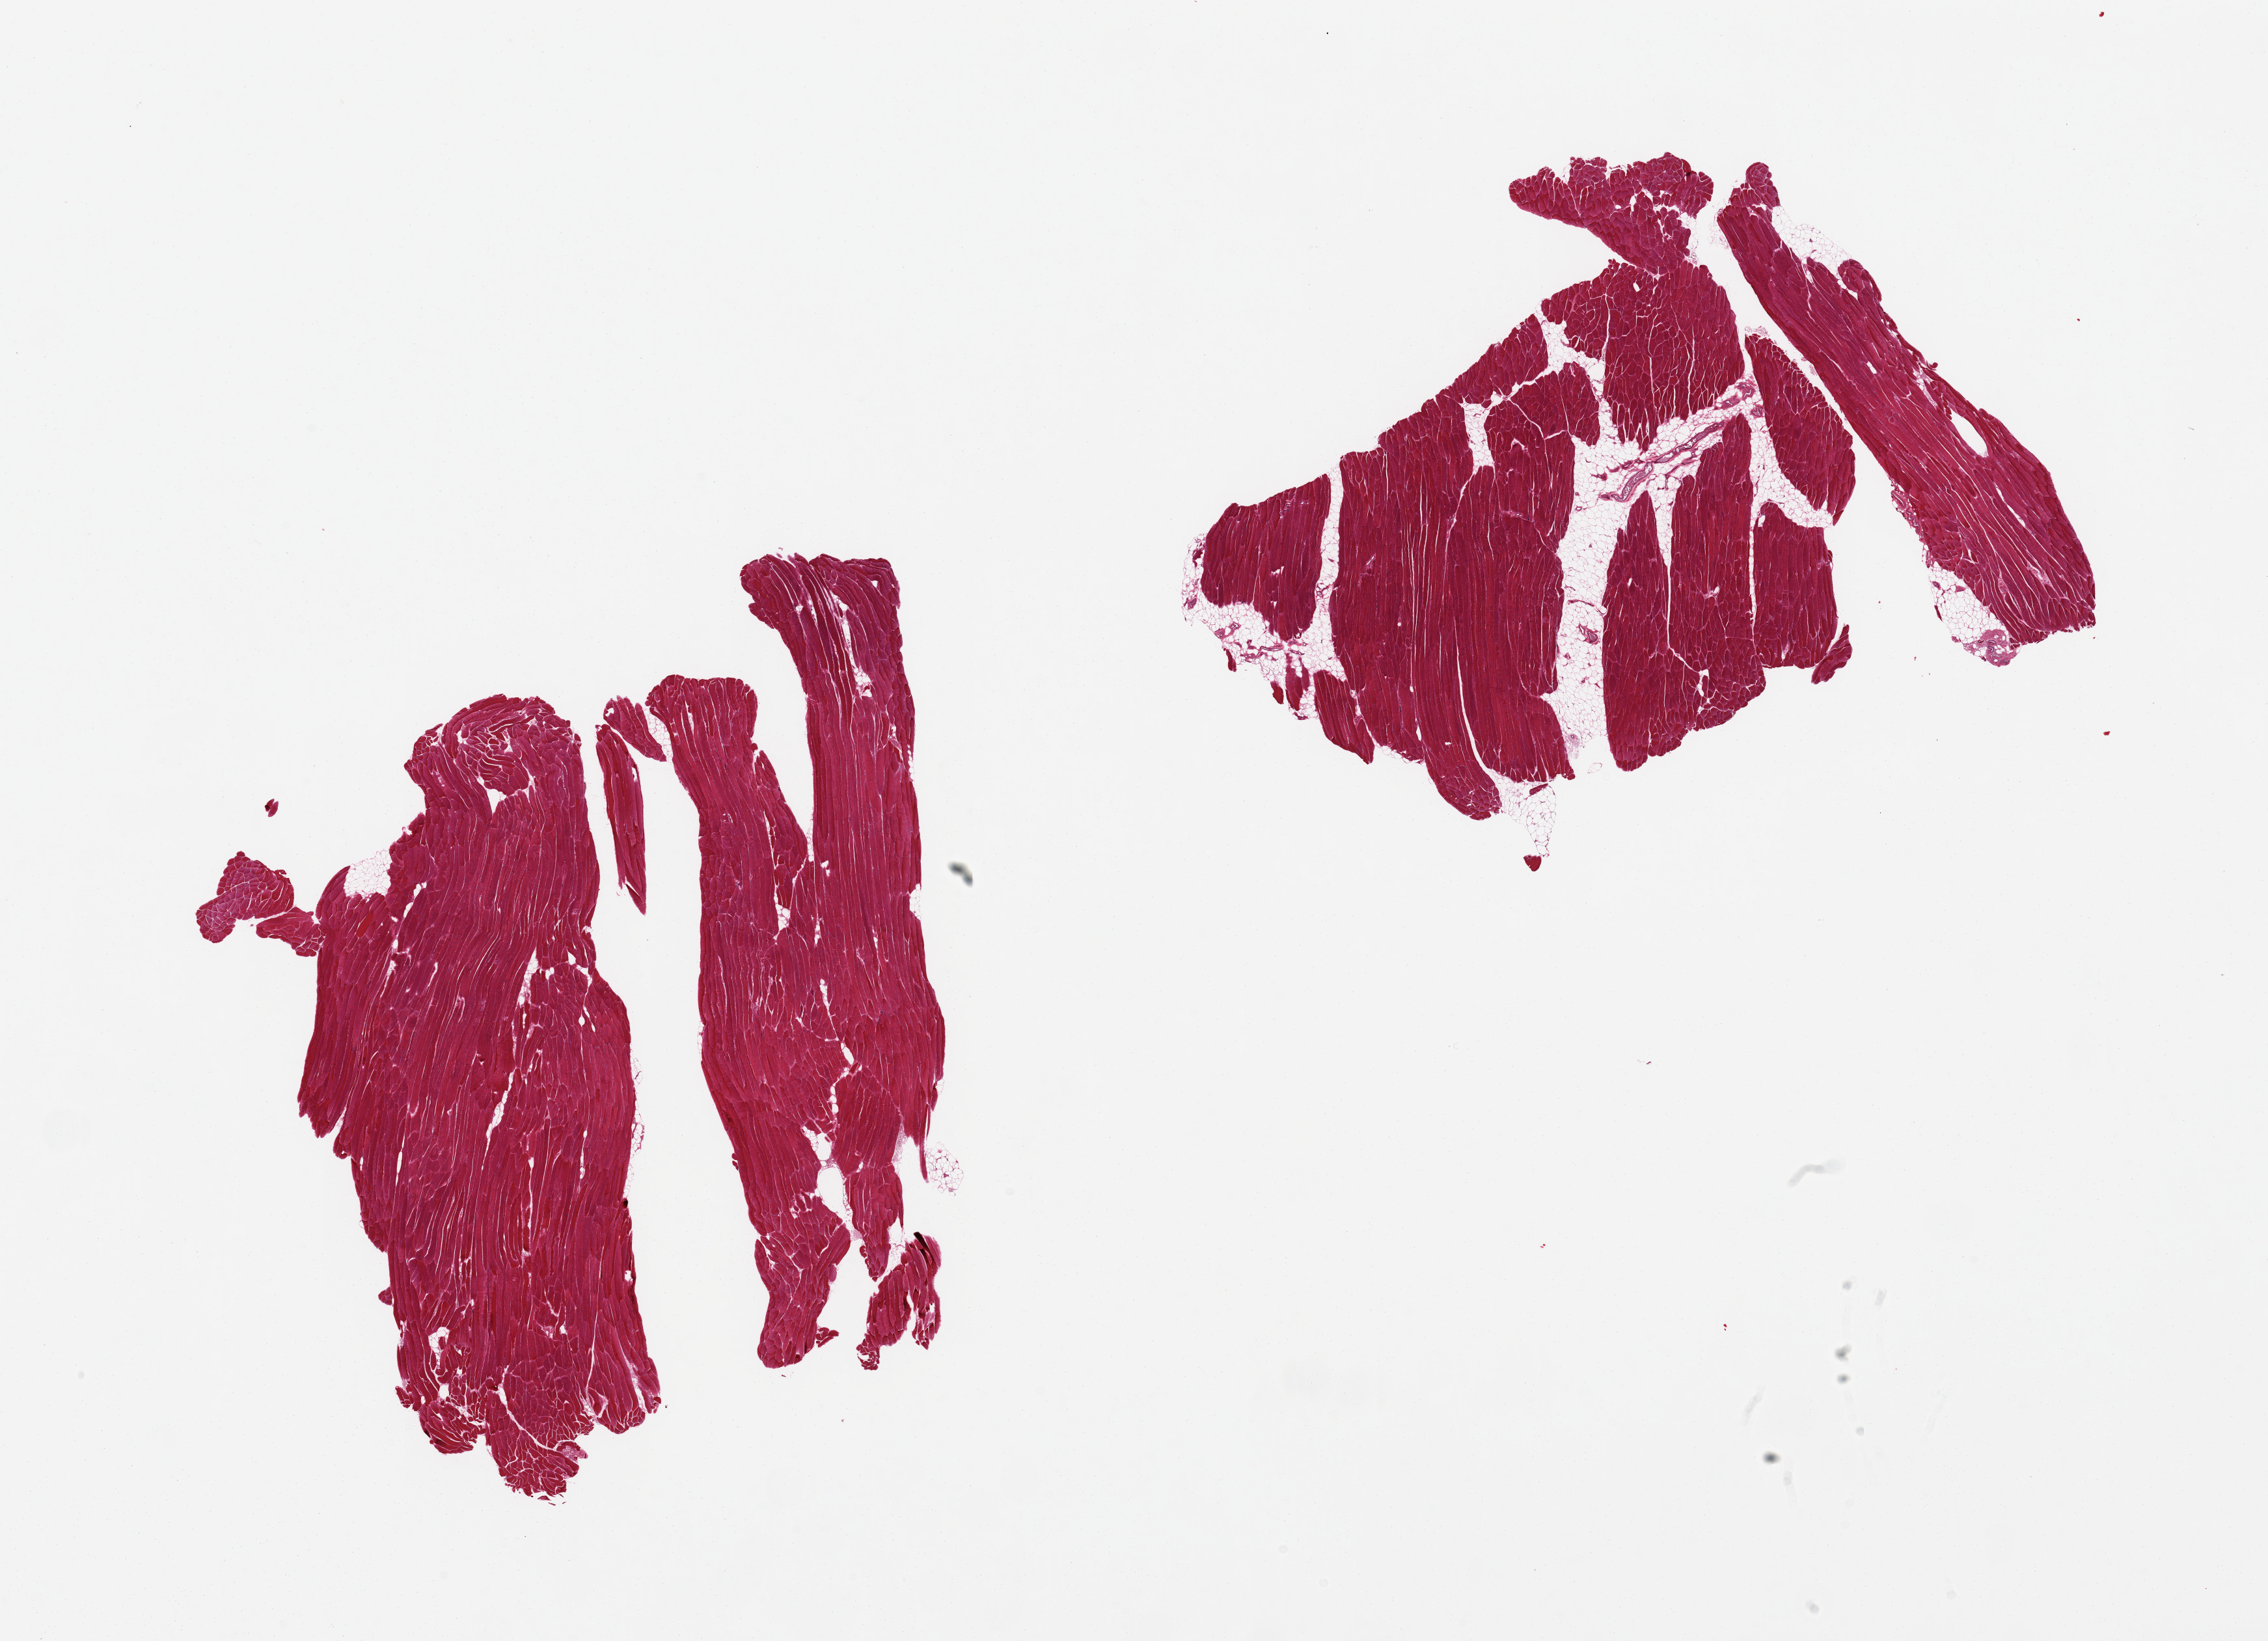
Digitized haematoxylin and eosin-stained section, shown as a low-resolution overview of the whole scanned area (about 27.6 x 19.9 mm, acquisition: 20x scan), PAXgene-fixed paraffin-embedded (PFPE) section, target tissue: skeletal muscle, donor tissue sample. Male donor.
Pathologist's review note for this sample: 2 pieces (fragmented), one includes ~20% fat (mostly internal).